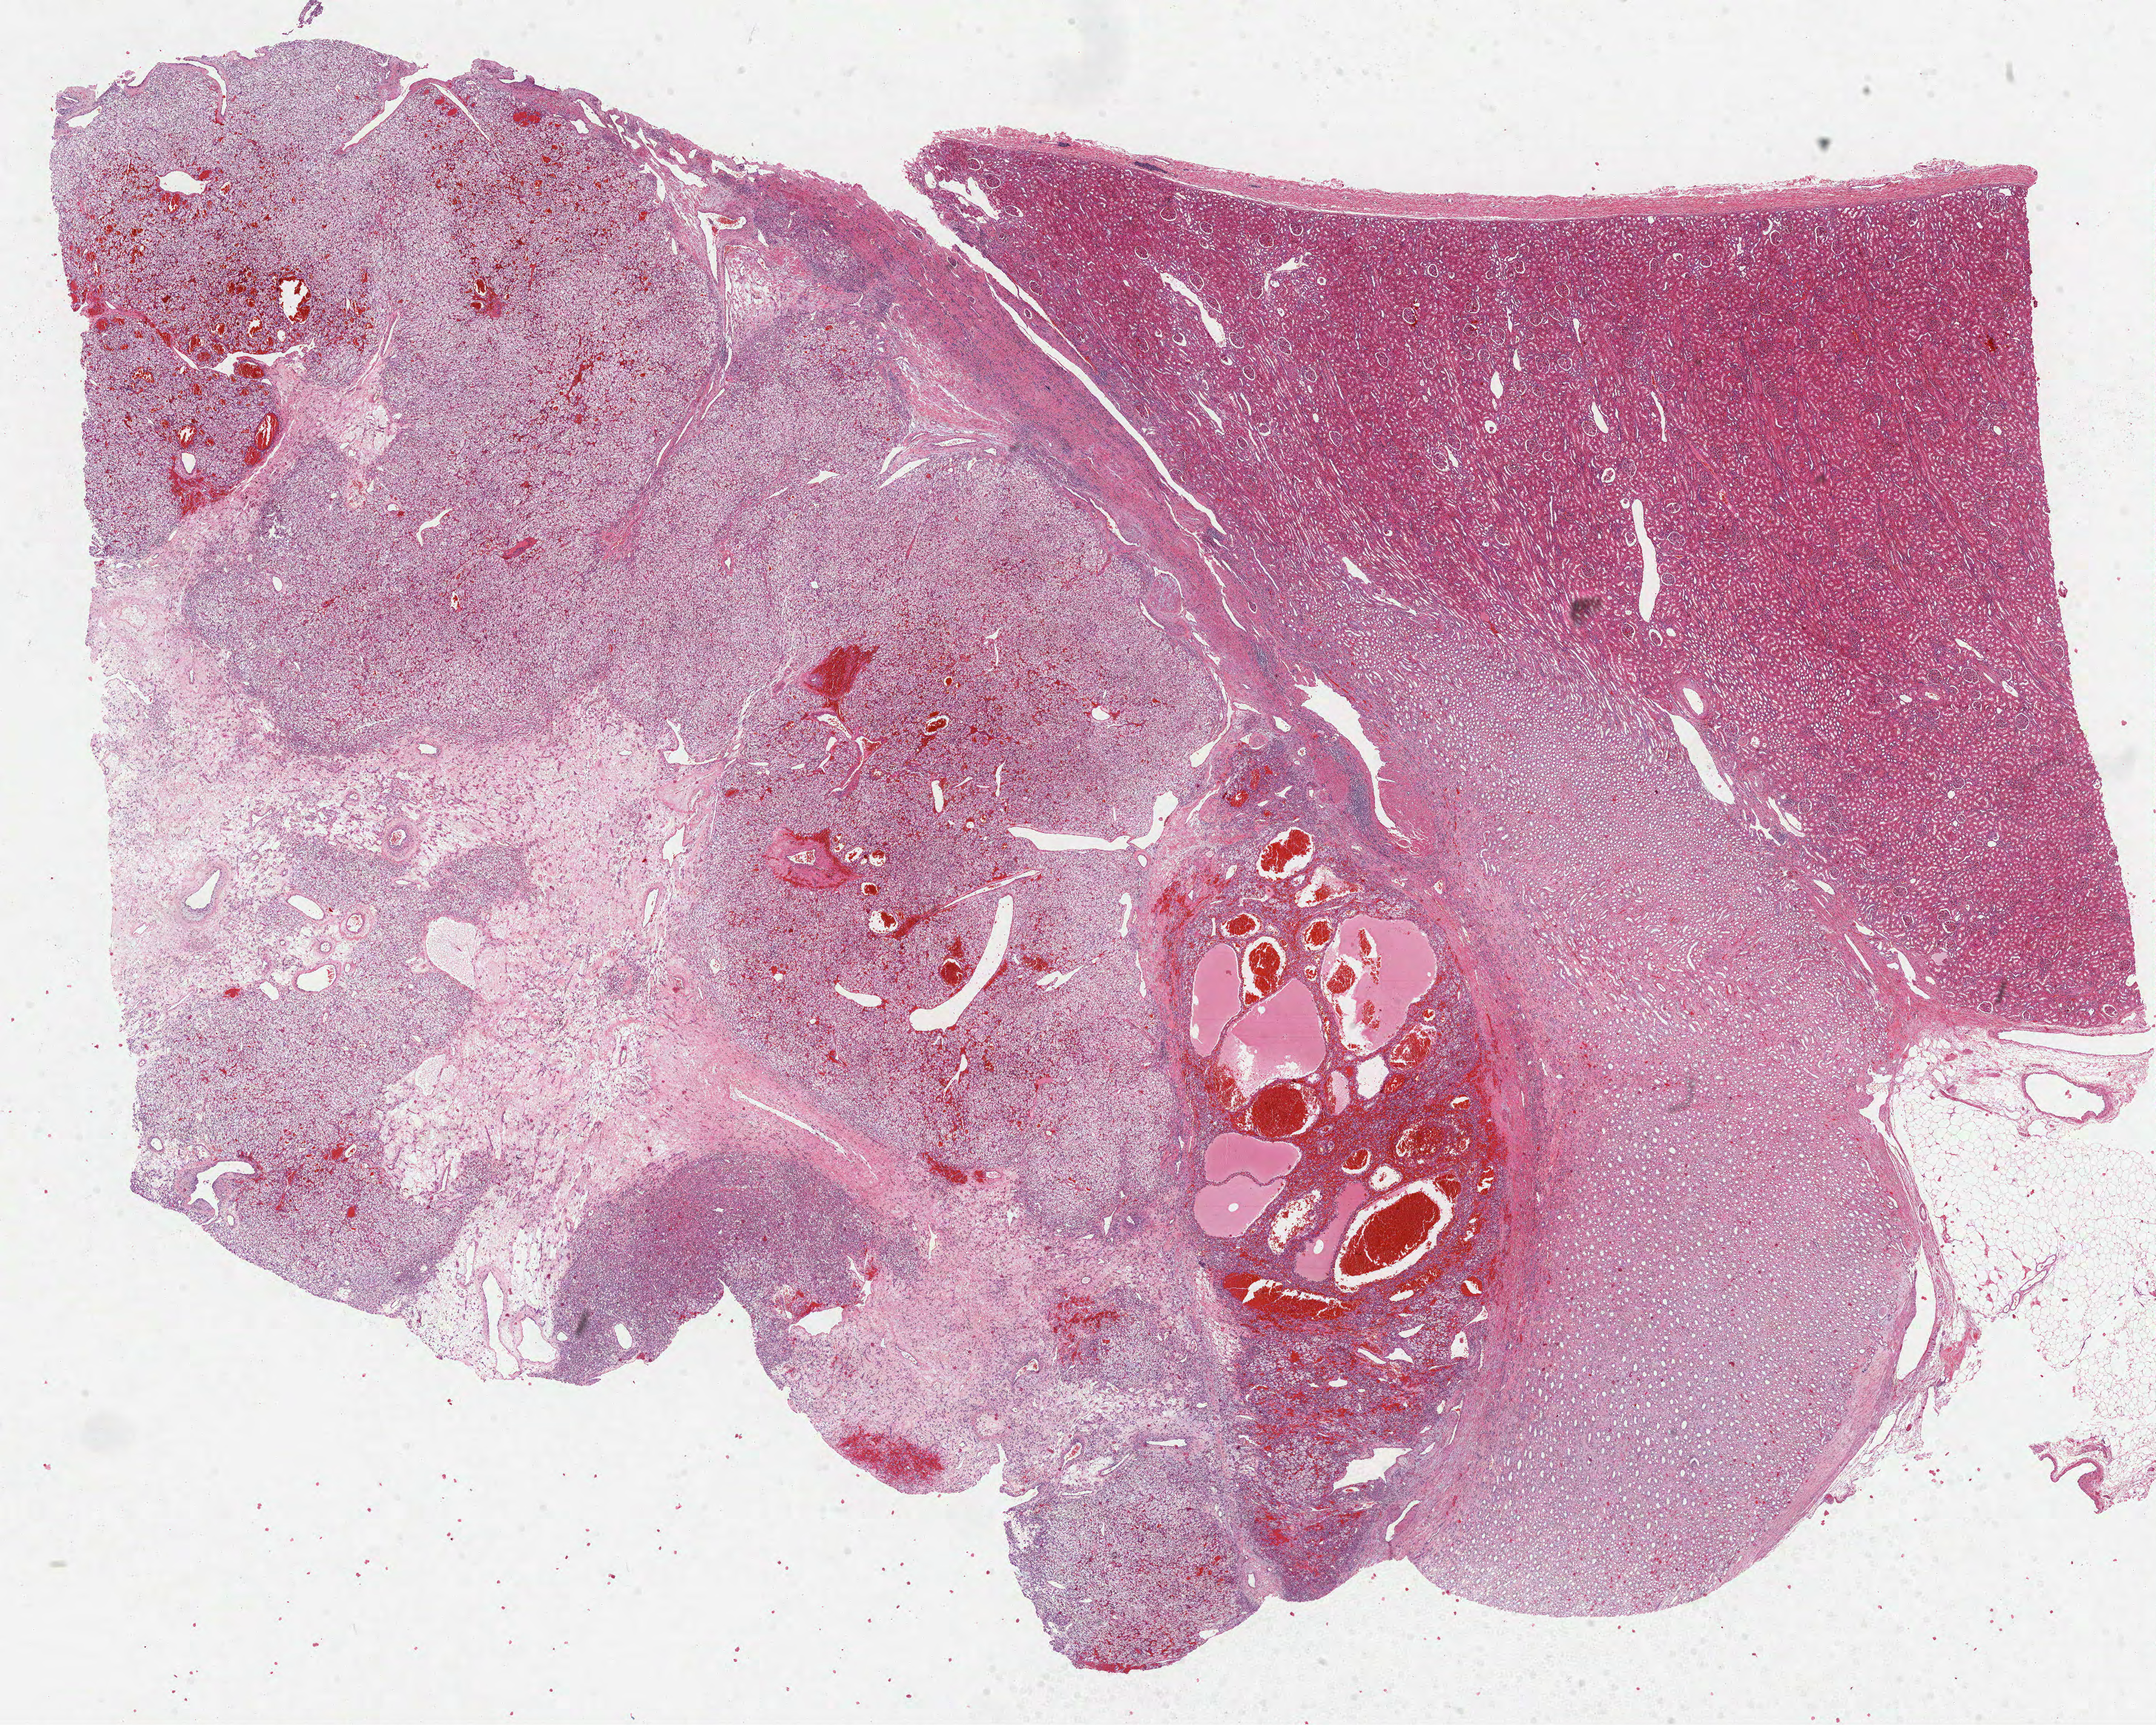
Whole-slide histology image, H&E-stained, shown as a low-resolution overview of the whole scanned area (about 23.4 x 18.8 mm). Formalin-fixed paraffin-embedded (FFPE) diagnostic section. Primary tumour sample from the kidney. Female patient; age at initial diagnosis 53 years. Histologic grade: G1 (well differentiated).
Histologic diagnosis: Clear cell adenocarcinoma, NOS. AJCC pathologic stage: I (6th edition). Laterality: right. TNM: T1b NX M0.